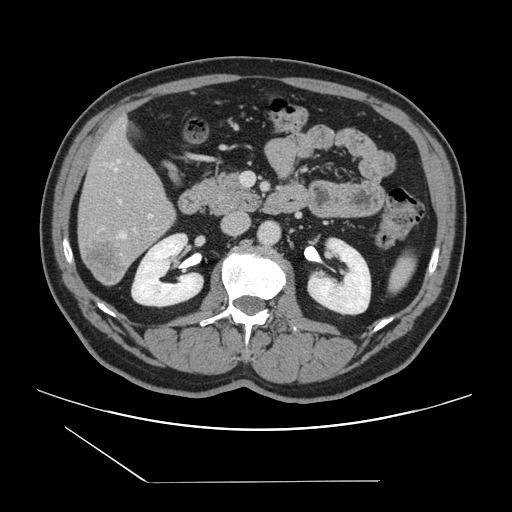
Contrast-enhanced abdominal CT, one axial slice. Position 58 of 157 along the scan axis. 120 kVp. Intravenous contrast given. Soft-tissue window (W 400 / L 40 HU). 2.5 mm slice thickness. 512 × 512 image matrix, field of view 407 × 407 mm. Male patient, age 61 years. From the clinical record (not read from this slice): diagnosis: colorectal cancer liver metastases, imaged before liver resection; multiple liver metastases: yes; largest metastasis: 5.5 cm.
Annotated regions visible in this slice (outlined manually by an expert reader):
- hepatic veins: box from (x=115, y=160) to (x=126, y=238) px
- liver: (x=79, y=121)–(x=175, y=285)
- planned liver remnant (the part of the liver to remain after resection): (x=80, y=121)–(x=169, y=218)
- portal vein (with intrahepatic branches): (x=101, y=200)–(x=153, y=229)
- liver metastasis: (x=84, y=242)–(x=124, y=284)